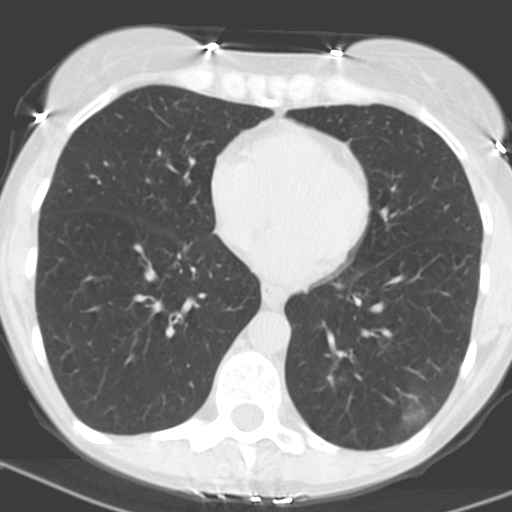
Chest CT (low-dose screening protocol), one axial image. First (baseline) screen. Lung window (W 1500 / L -600 HU). 3.2 mm slice thickness. Slice 95 of 156 in the series. Female participant, aged 56 years at enrolment.
Expert reader's lesion annotation, bounding box [x1, y1, x2, y2] px = [367, 367, 451, 442]. The exam's reader record, not a measurement of the box and not confirmed to be the same lesion: non-calcified nodule or mass ≥4 mm, left lower lobe, 31 × 23 mm, poorly defined margins, soft tissue attenuation, pre-existing on the prior screen: no. Later outcome: lung cancer diagnosed 27 days after this screen — squamous cell carcinoma, NOS, left lower lobe, poorly differentiated (G3), stage IB (AJCC 6th edition), 35 mm at pathology.